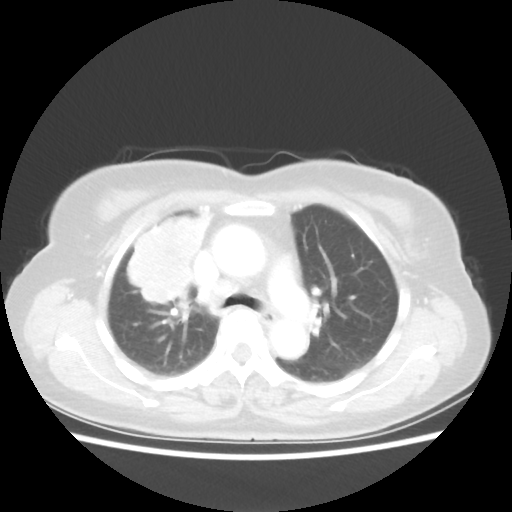
Chest CT, one axial slice. Position 36 of 55 along the scan axis. Lung window (W 1500 / L -600 HU). 5 mm slice thickness. 512 × 512 image matrix, field of view 337 × 337 mm. Patient: female, 62 years. Case-level facts recorded for this patient, not image findings: clinical TNM (as recorded): T4 N3 M0.
Annotated regions visible in this slice (bounding box drawn by a radiologist):
- lung tumour (recorded histology: squamous cell carcinoma): bounding box <110,203,209,306> (left, top, right, bottom; pixels)